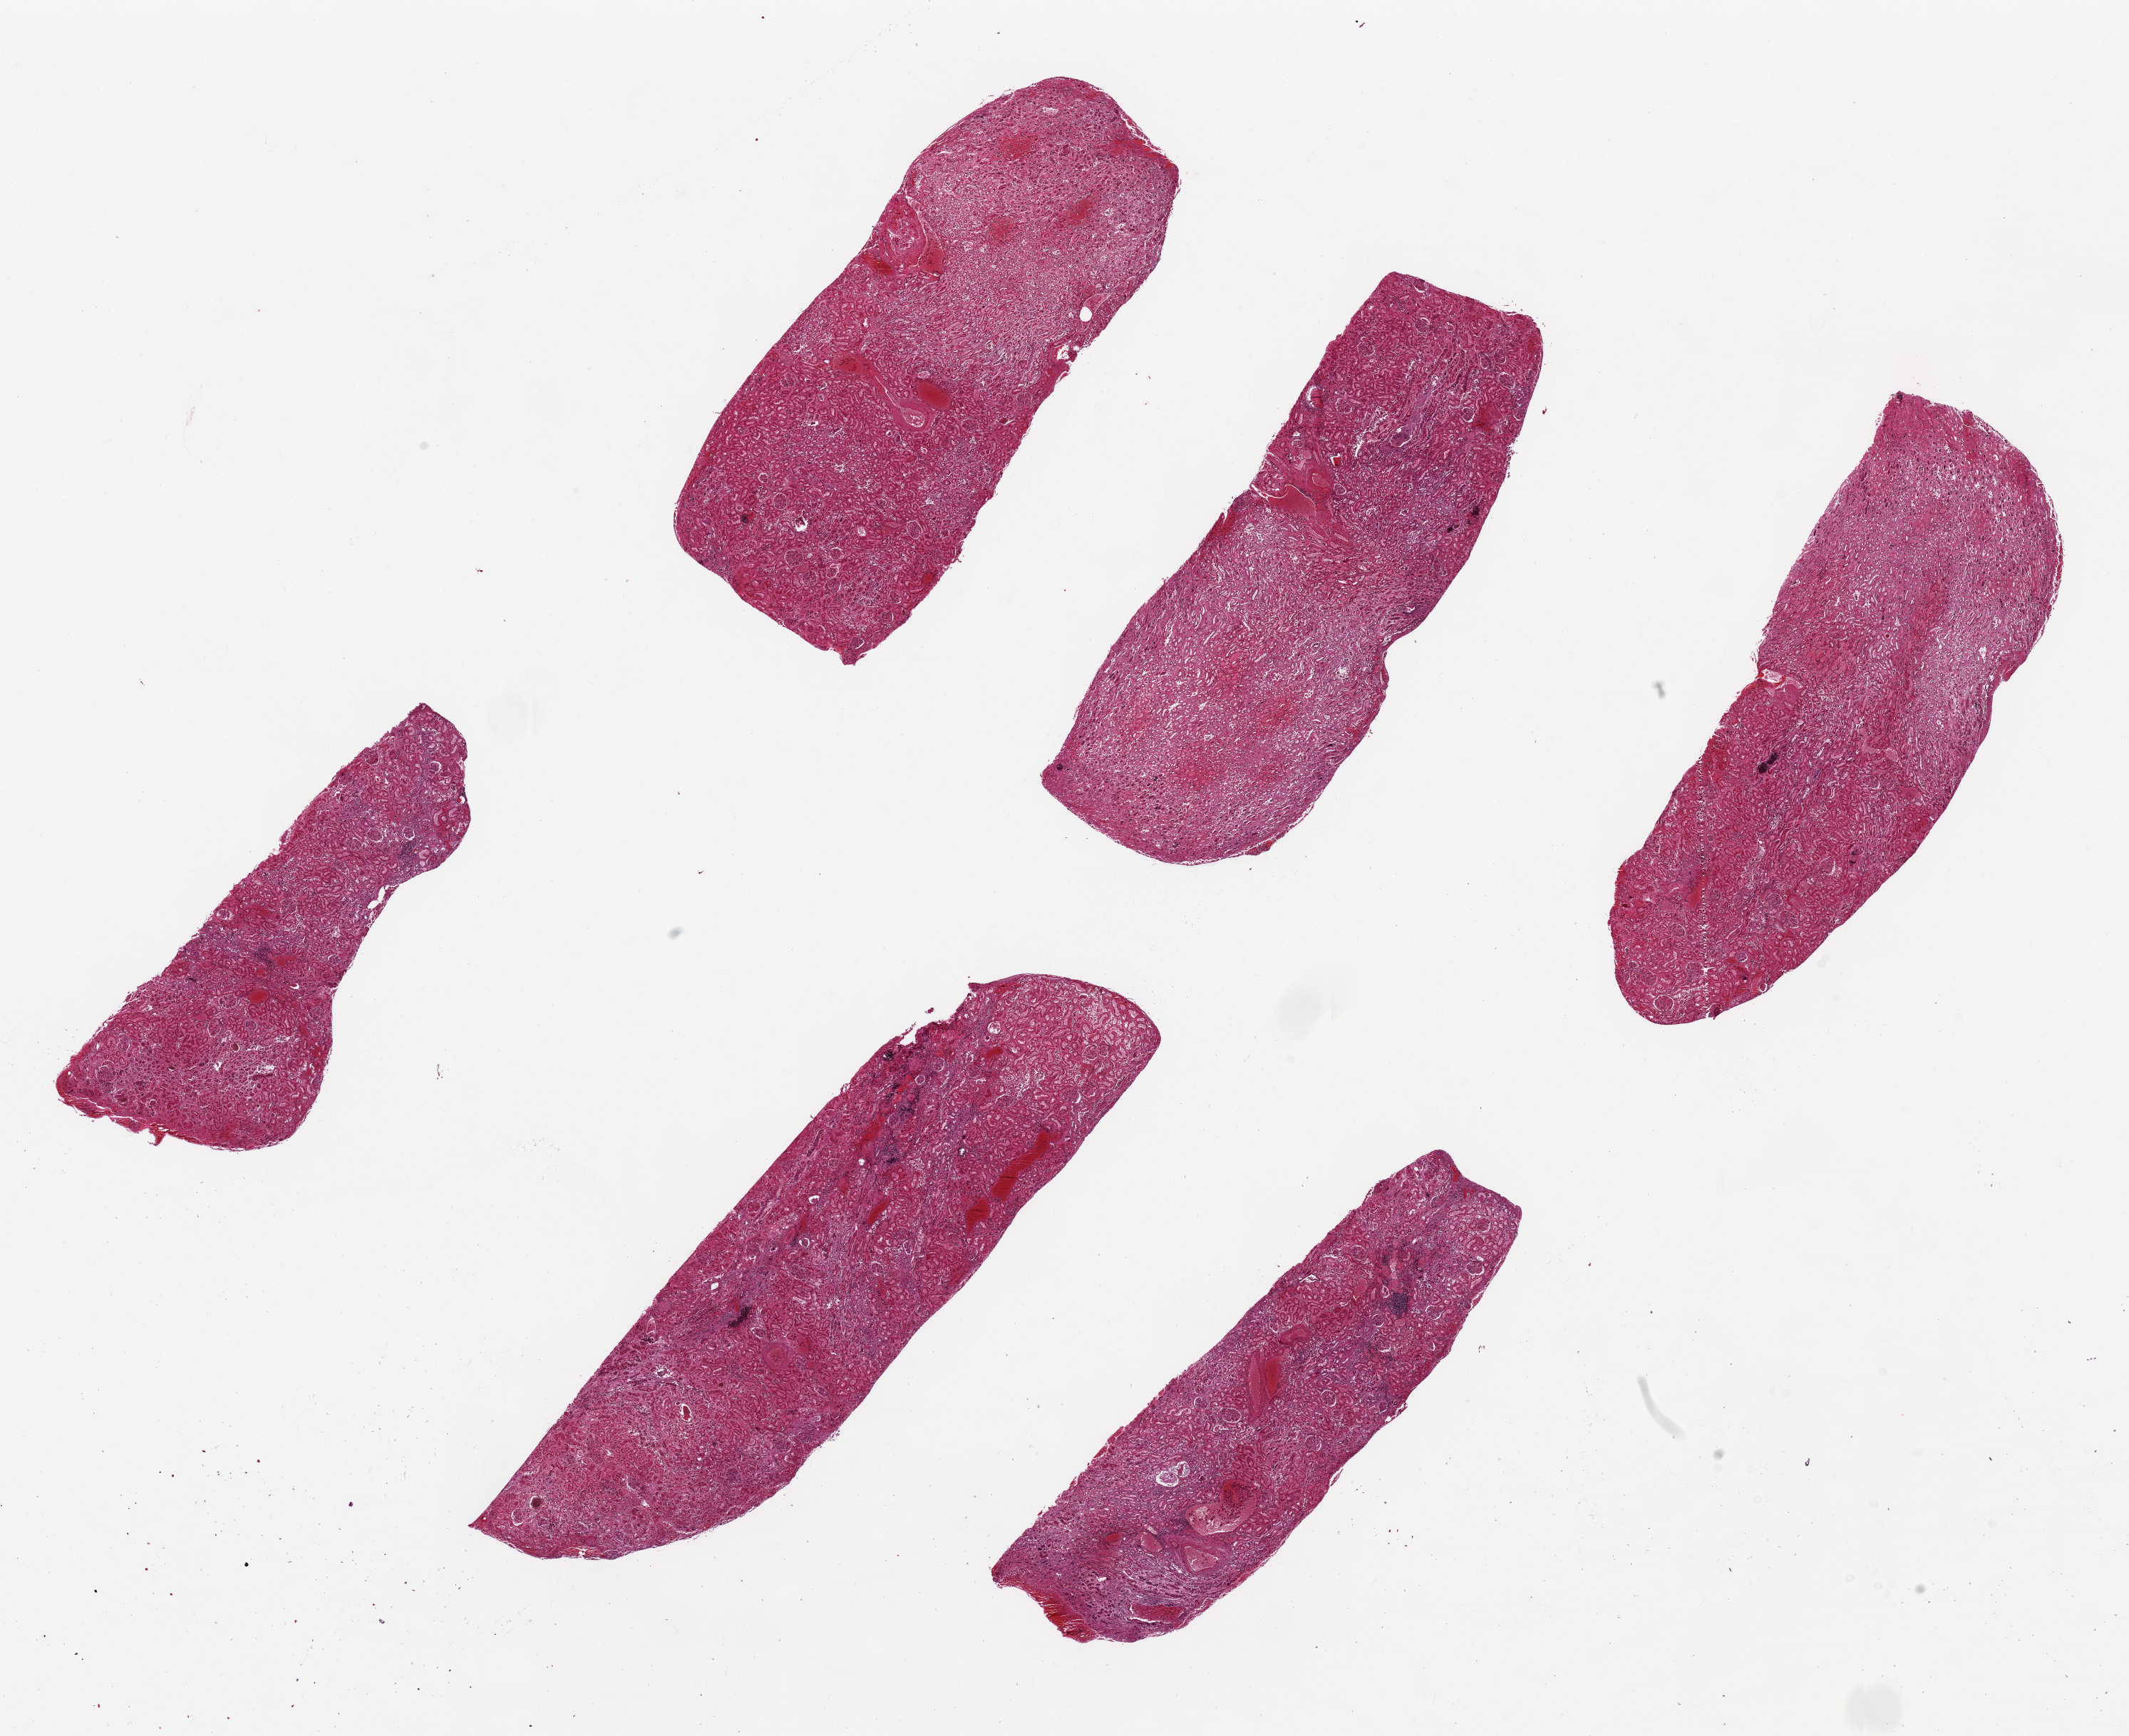
Haematoxylin and eosin whole-slide image — shown as a low-resolution overview of the whole scanned area (about 23.6 x 19.3 mm), PAXgene-fixed, paraffin-embedded tissue, target tissue: renal cortex, tissue donor sample.
Pathologist's review note for this sample: 6 pieces, ~7x2.5mm. Tubules badly autolyzed. Patchy interstitial inflammation, abundant crystaloid deposits in tubular lumina ? origin.